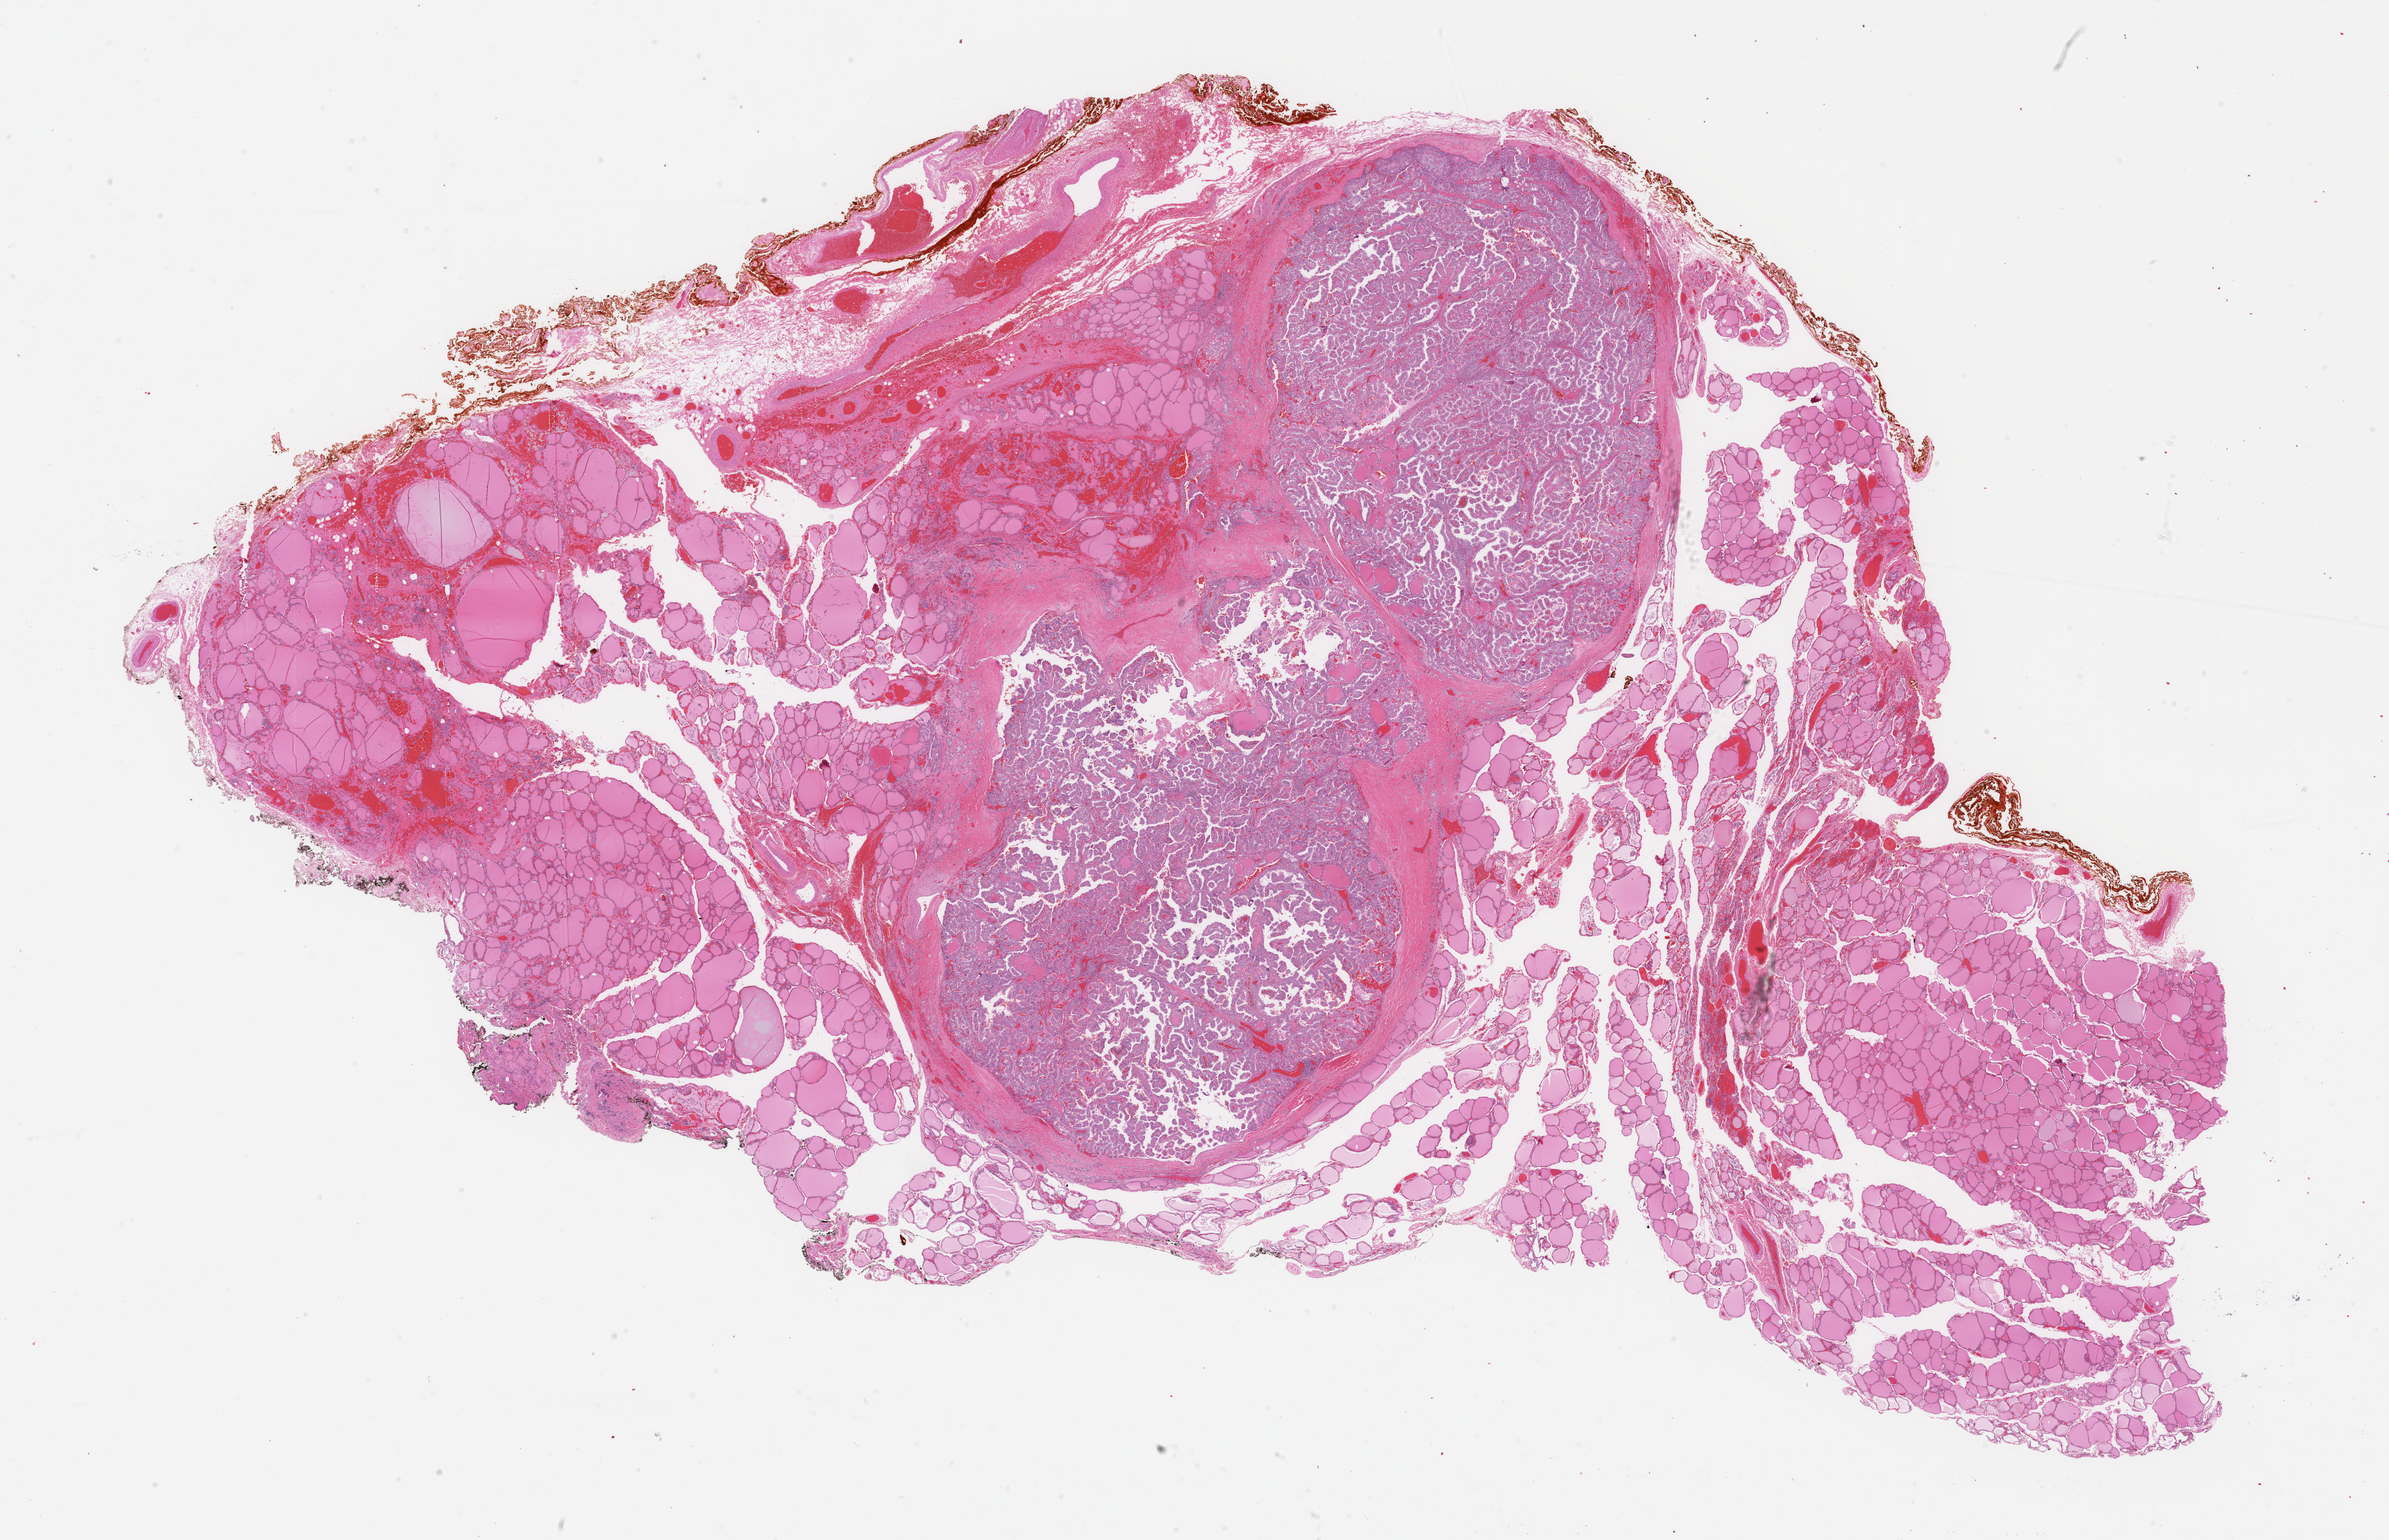
Digitized Hematoxylin and eosin (H&E) stained tissue section (whole slide), low-resolution overview of the scanned area, about 29.7 x 19.2 mm; formalin-fixed paraffin-embedded (FFPE) diagnostic section; thyroid, primary tumour sample. Patient: male, age at initial diagnosis 28 years.
* lymph nodes positive (case pathology): 6 of 9 examined
* AJCC pathologic stage: I (6th edition)
* histologic diagnosis: Papillary adenocarcinoma, NOS (thyroid gland)